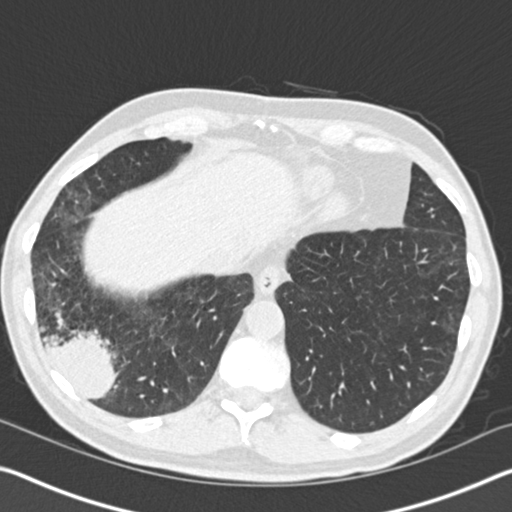
Axial slice from a low-dose chest CT screening exam, first (baseline) screen, lung window (W 1500 / L -600 HU), standard (soft-tissue) reconstruction kernel (B30f). Male, age 61 years at enrolment. Current smoker at enrolment.
- Expert-annotated lung lesion, bounding box [x1, y1, x2, y2] px = [13, 279, 138, 415].
- The exam's reader record, not a measurement of the box and not confirmed to be the same lesion: non-calcified nodule or mass ≥4 mm, right lower lobe, 52 × 36 mm, spiculated (stellate) margins, soft tissue attenuation.